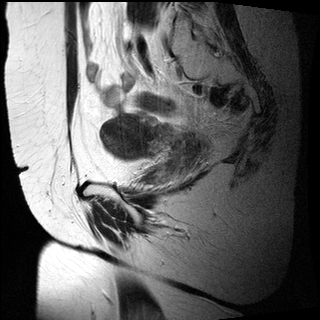
Pelvic MRI for cervical cancer, one sagittal slice. Slice 20 of 27 in the series (ordered by position). T2-weighted. 1.5 T. TE 89 ms, TR 2740 ms. 4 mm slice thickness. 320 × 320 image matrix, field of view 260 × 260 mm. Female patient, age 47 years.
Annotated regions visible in this slice (manually delineated by an expert):
- uterus and cervix: bounding box (x1, y1, x2, y2) in pixels: (100, 115, 203, 167)